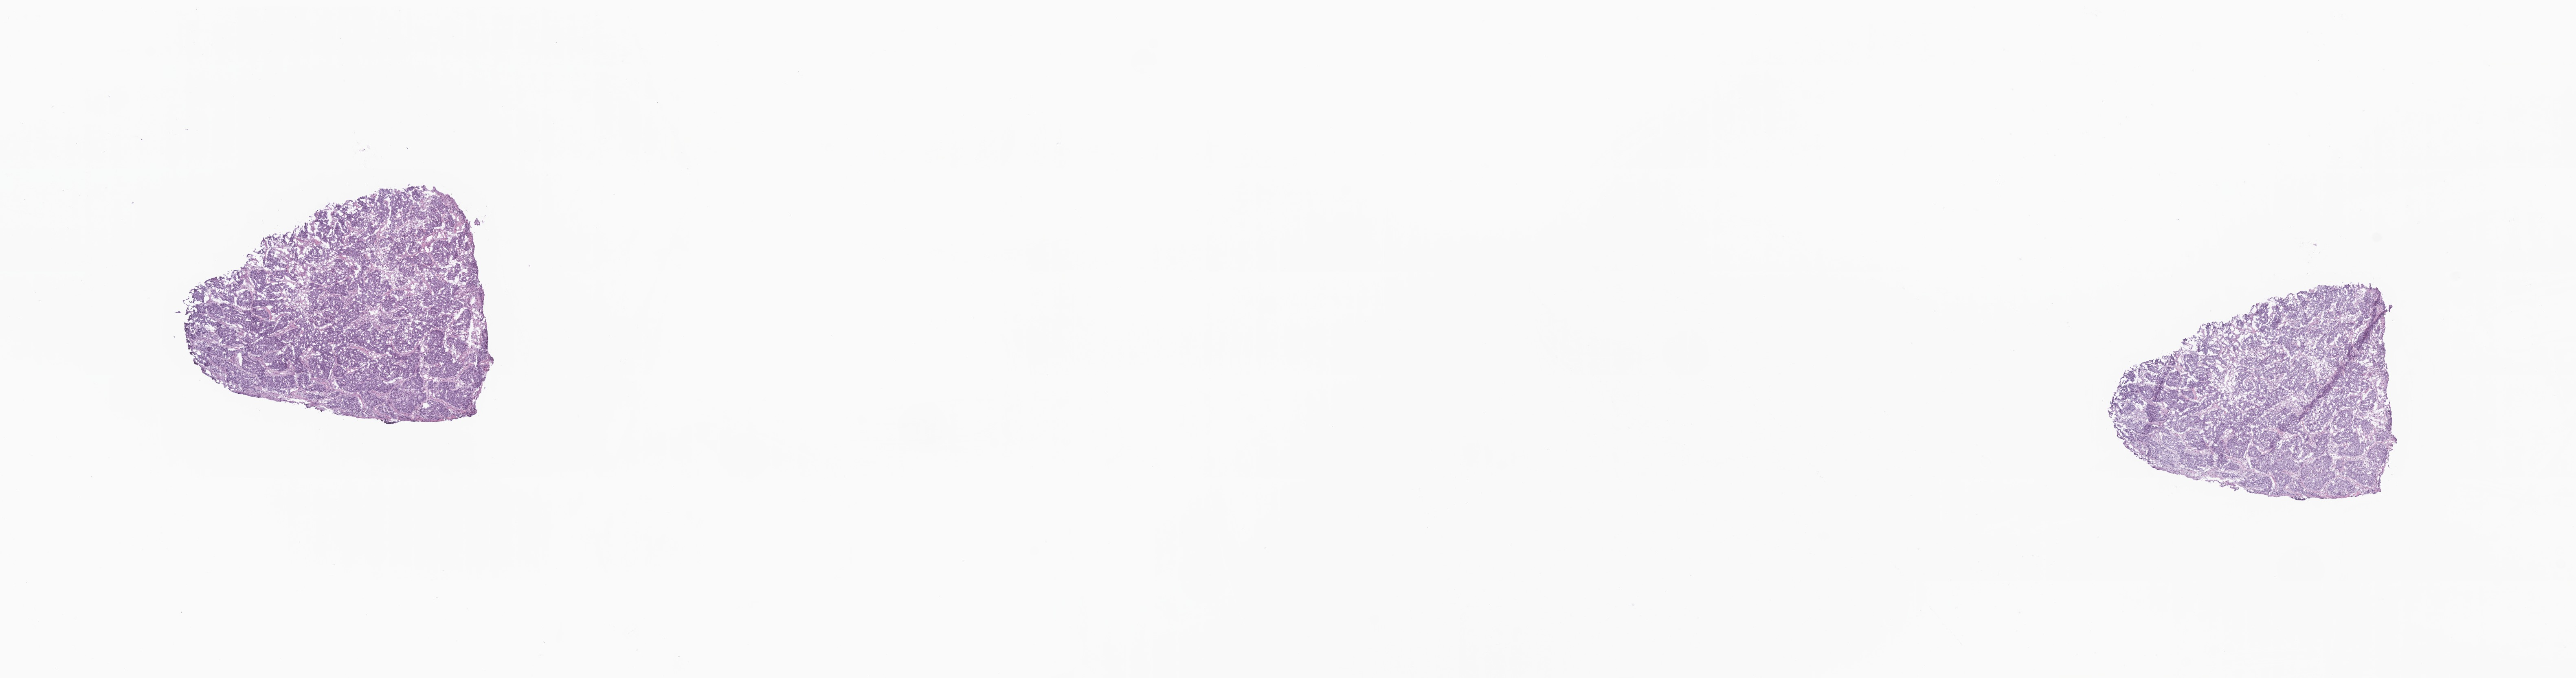
Digitized H&E-stained section, a low-resolution overview of the entire scanned area, about 26.7 x 7.0 mm. Frozen section. Primary tumor. Anatomic site: breast. Patient: female, age at initial diagnosis 62 years. Slide review estimates, as recorded: tumor cells 85%, tumor nuclei 90%, stromal cells 15%, necrosis 0%, normal cells 0%. Inflammatory infiltration, as recorded: lymphocyte infiltration 0%, monocyte infiltration 0%, neutrophil infiltration 0%.
Diagnosis: Infiltrating duct carcinoma, NOS.